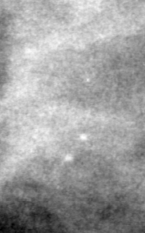
Region of interest cut from a scanned film mammogram (one marked finding); left breast; CC view.
- Calcifications, morphology pleomorphic, distribution clustered; BI-RADS assessment category 4; subtlety rating 1 on a 1 (subtle) to 5 (obvious) scale; pathology result (as recorded, not read from the image): malignant.